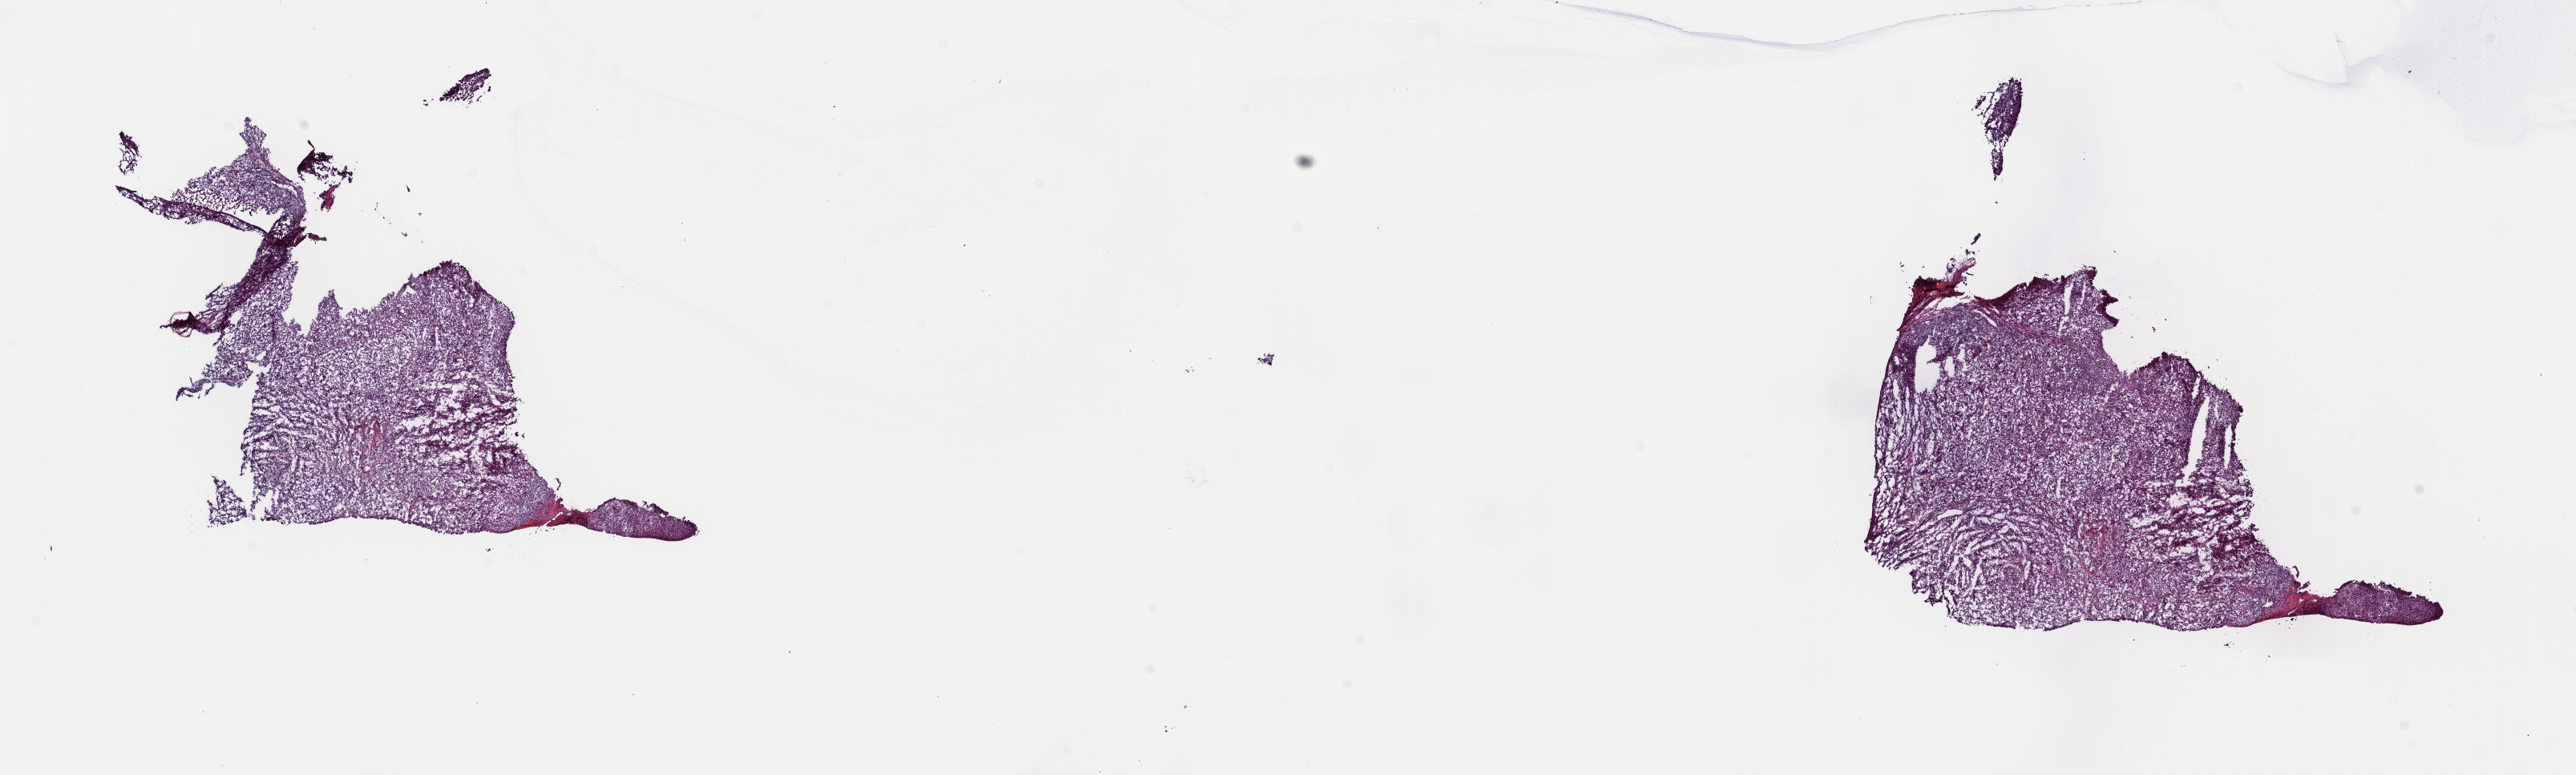
H&E whole-slide image, low-resolution overview of the scanned area, about 25.4 x 7.6 mm; frozen section; metastatic tumour sample, sampled site not recorded. Patient: male, age at initial diagnosis 19 years. Pathologist review of this section (percent, as recorded): tumour cells 100%, tumour nuclei 85%, normal cells 0%, stromal cells 0%, necrosis 0%. Infiltration values recorded for this section: lymphocyte infiltration 2%, monocyte infiltration 1%, neutrophil infiltration 0%.
- this section: metastatic tumour tissue
- patient diagnosis: Malignant melanoma, NOS